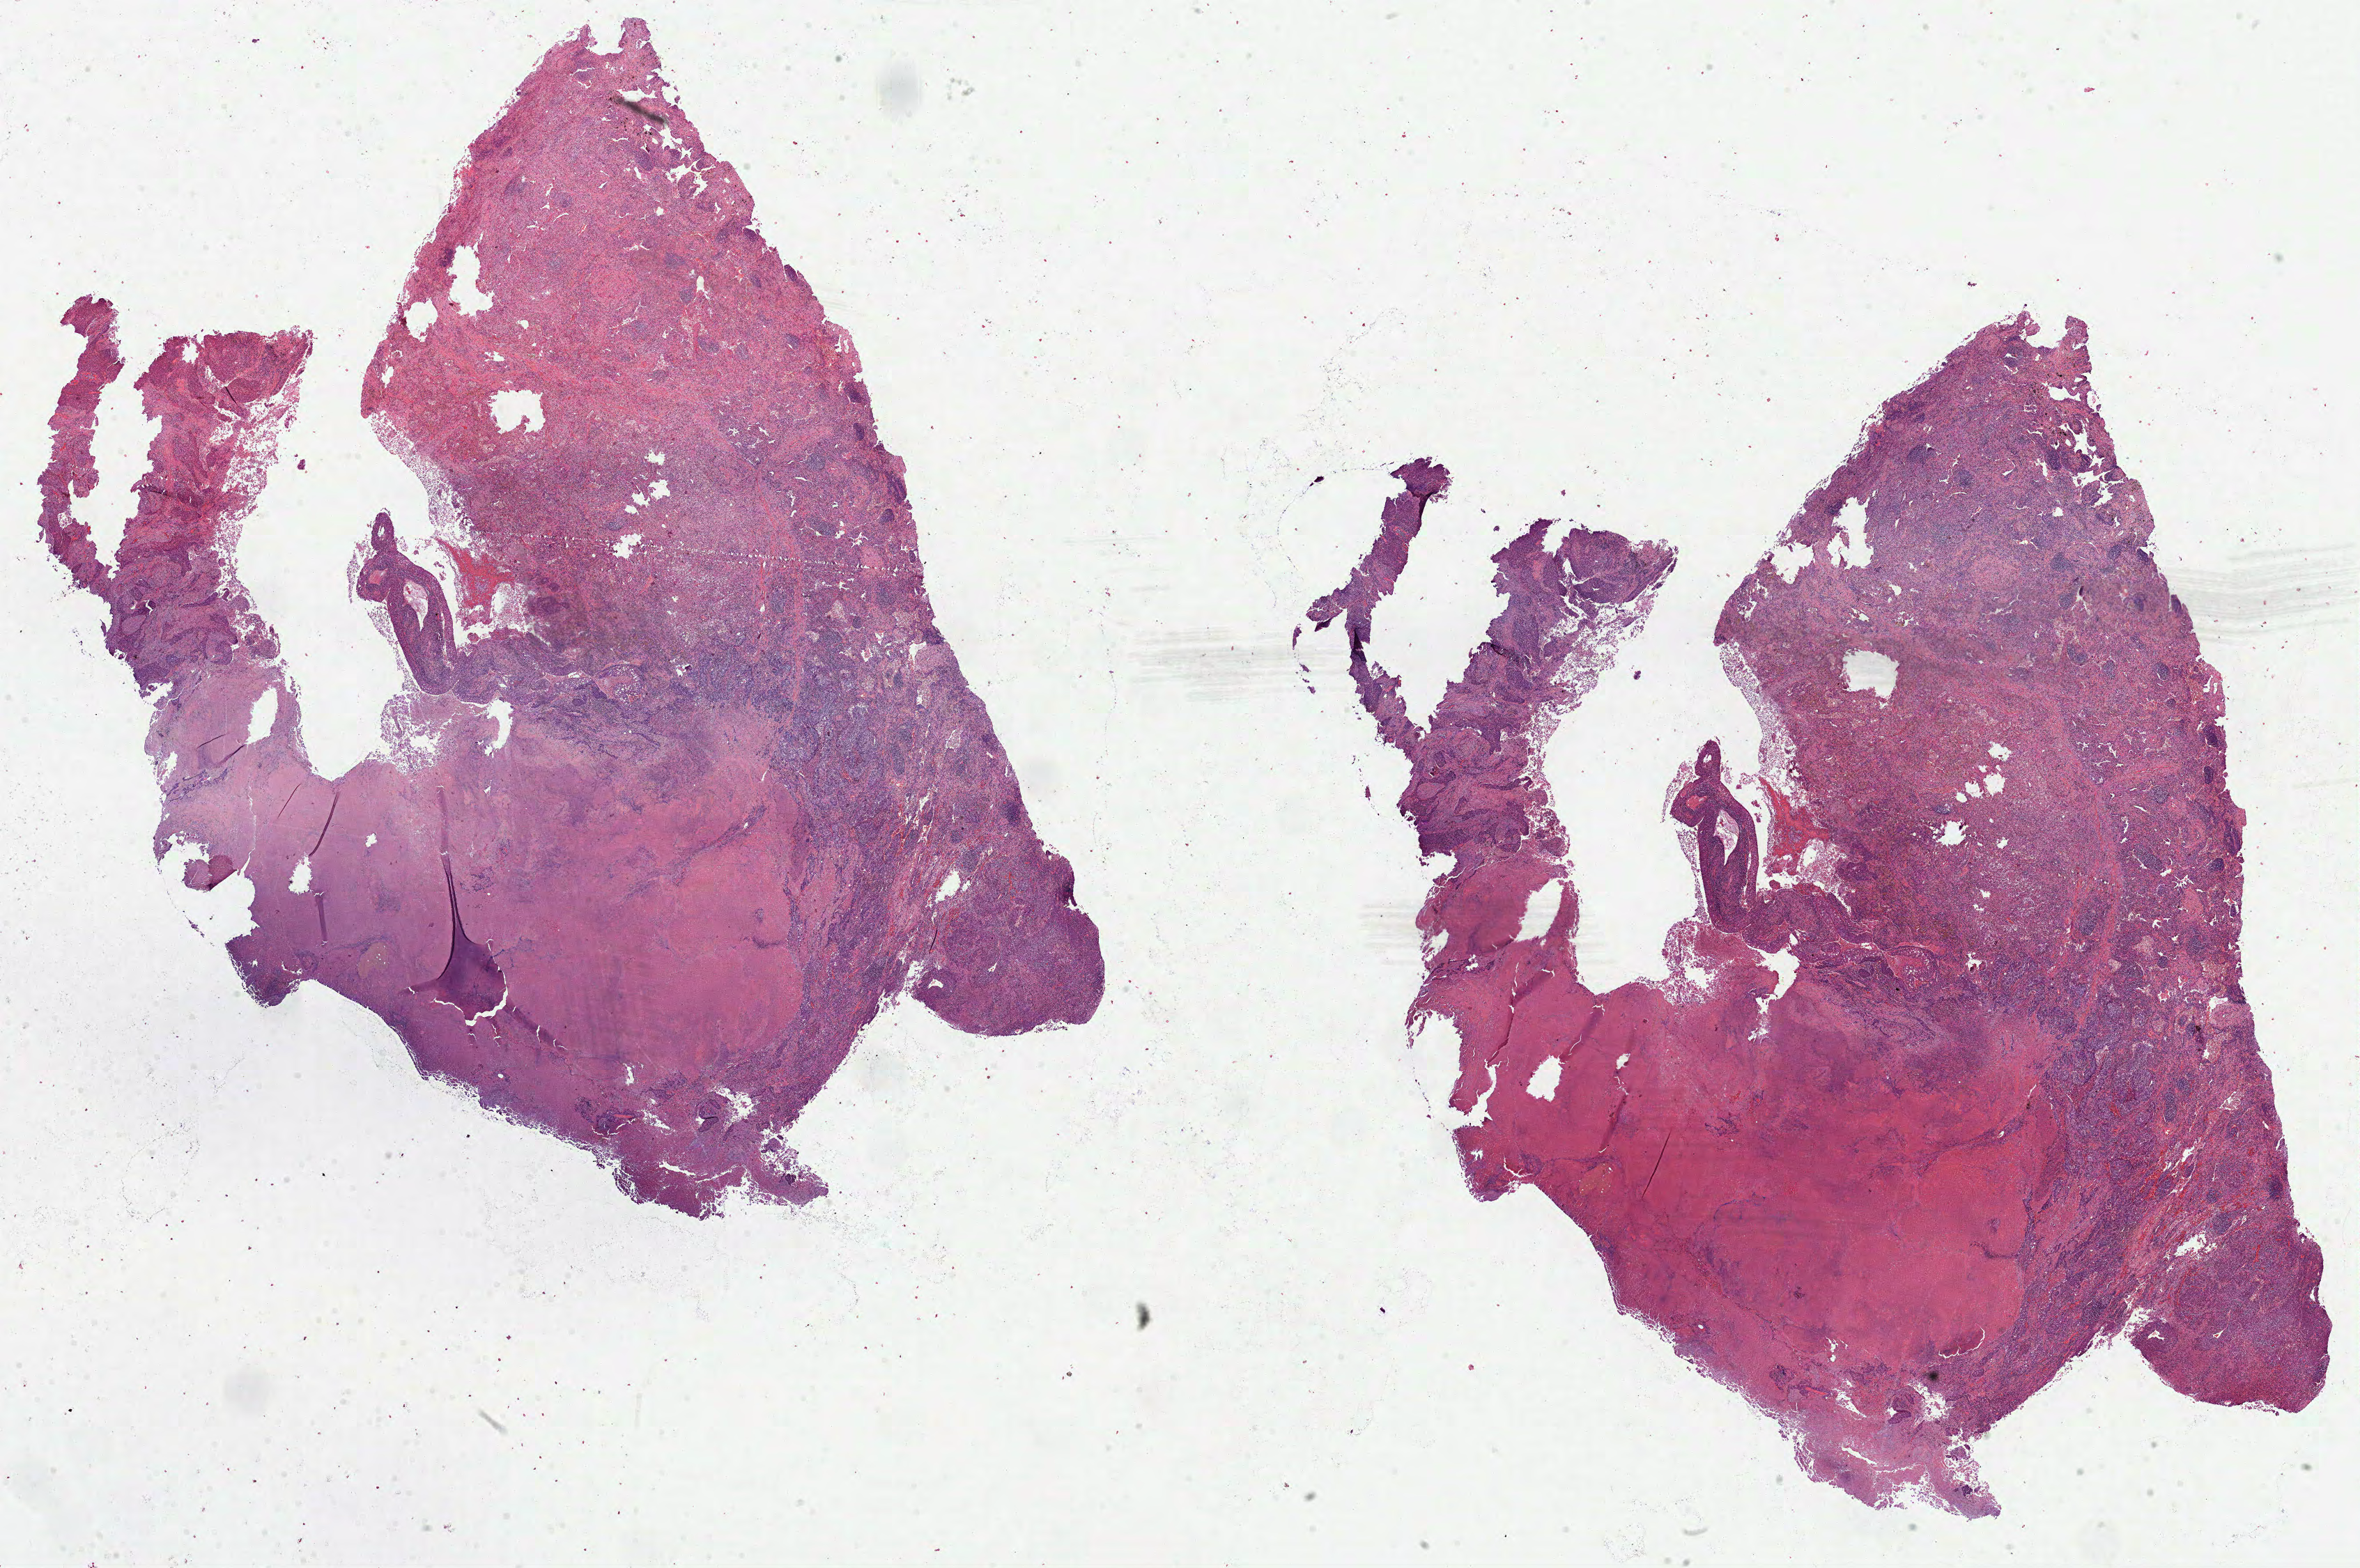
Whole-slide histology image, Hematoxylin and eosin (H&E) stained — low-resolution overview of the scanned area, about 27.3 x 18.2 mm. Formalin-fixed paraffin-embedded (FFPE) diagnostic section. Primary tumour sample from the lung. Patient: male, age at initial diagnosis 70 years.
Laterality: right. AJCC pathologic stage: IIIA. TNM: T3 N1 M0. Histologic diagnosis: Squamous cell carcinoma, NOS.